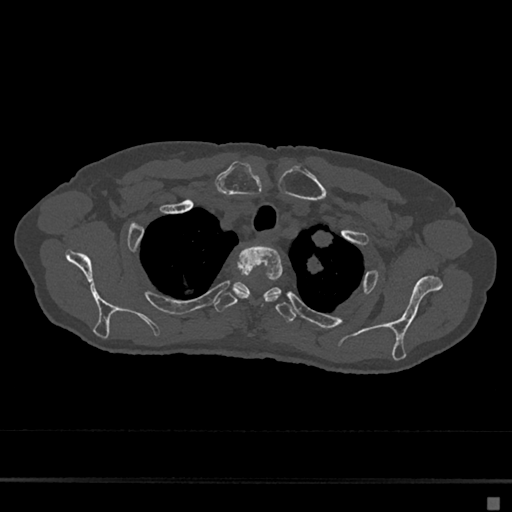
CT including the spine, one axial slice; slice 562 of 797 in the series (ordered by position); 120 kVp; bone window (W 1800 / L 400 HU); 0.5 mm slice thickness; 512 × 512 image matrix. Patient: female, 68 years. From the clinical record (not read from this slice): primary cancer: renal.
Outlined on this slice (semi-automatically segmented with operator editing):
- T2 vertebra: bounding box (x1, y1, x2, y2) in pixels: (233, 245, 283, 303)
- T3 vertebra: (213, 282, 297, 322)